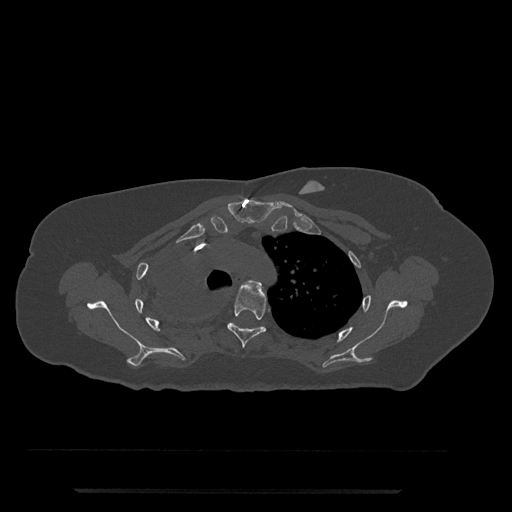
CT including the spine, one axial slice; slice 589 of 797 in the series (ordered by position); reconstruction kernel Br40s/3; bone window (W 1800 / L 400 HU); 512 × 512 image matrix. Patient: female, 51 years. Case-level facts recorded for this patient, not image findings: primary cancer: neuro.
Annotated regions visible in this slice (semi-automatically segmented with operator editing):
- T3 vertebra: bounding box (x1, y1, x2, y2) in pixels: (242, 280, 263, 290)
- T4 vertebra: (227, 285, 266, 348)
- T5 vertebra: (231, 323, 260, 329)